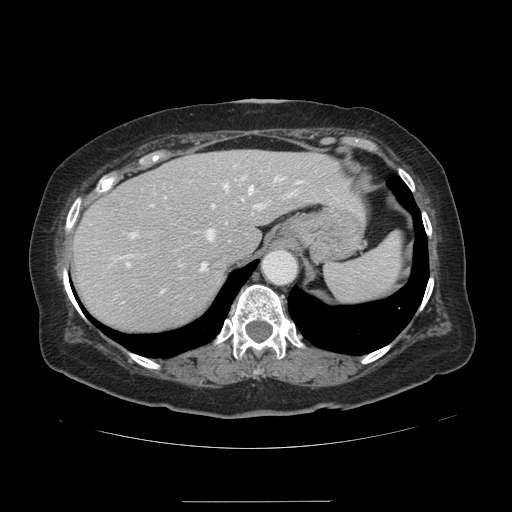
Contrast-enhanced abdominal CT, one axial slice; position 101 of 141 along the scan axis; intravenous contrast given; soft-tissue window (W 400 / L 40 HU); 2.5 mm slice thickness; 512 × 512 image matrix, field of view 393 × 393 mm. Female patient, age 74 years. Case-level facts recorded for this patient, not image findings: diagnosis: colorectal cancer liver metastases, imaged before liver resection; multiple liver metastases: yes; largest metastasis: 7 cm.
Structures marked on this image (outlined manually by an expert reader):
- hepatic veins: bounding box (x1, y1, x2, y2) in pixels: (110, 177, 300, 272)
- liver: (74, 150, 363, 333)
- planned liver remnant (the part of the liver to remain after resection): (76, 150, 363, 332)
- portal vein (with intrahepatic branches): (127, 176, 294, 293)